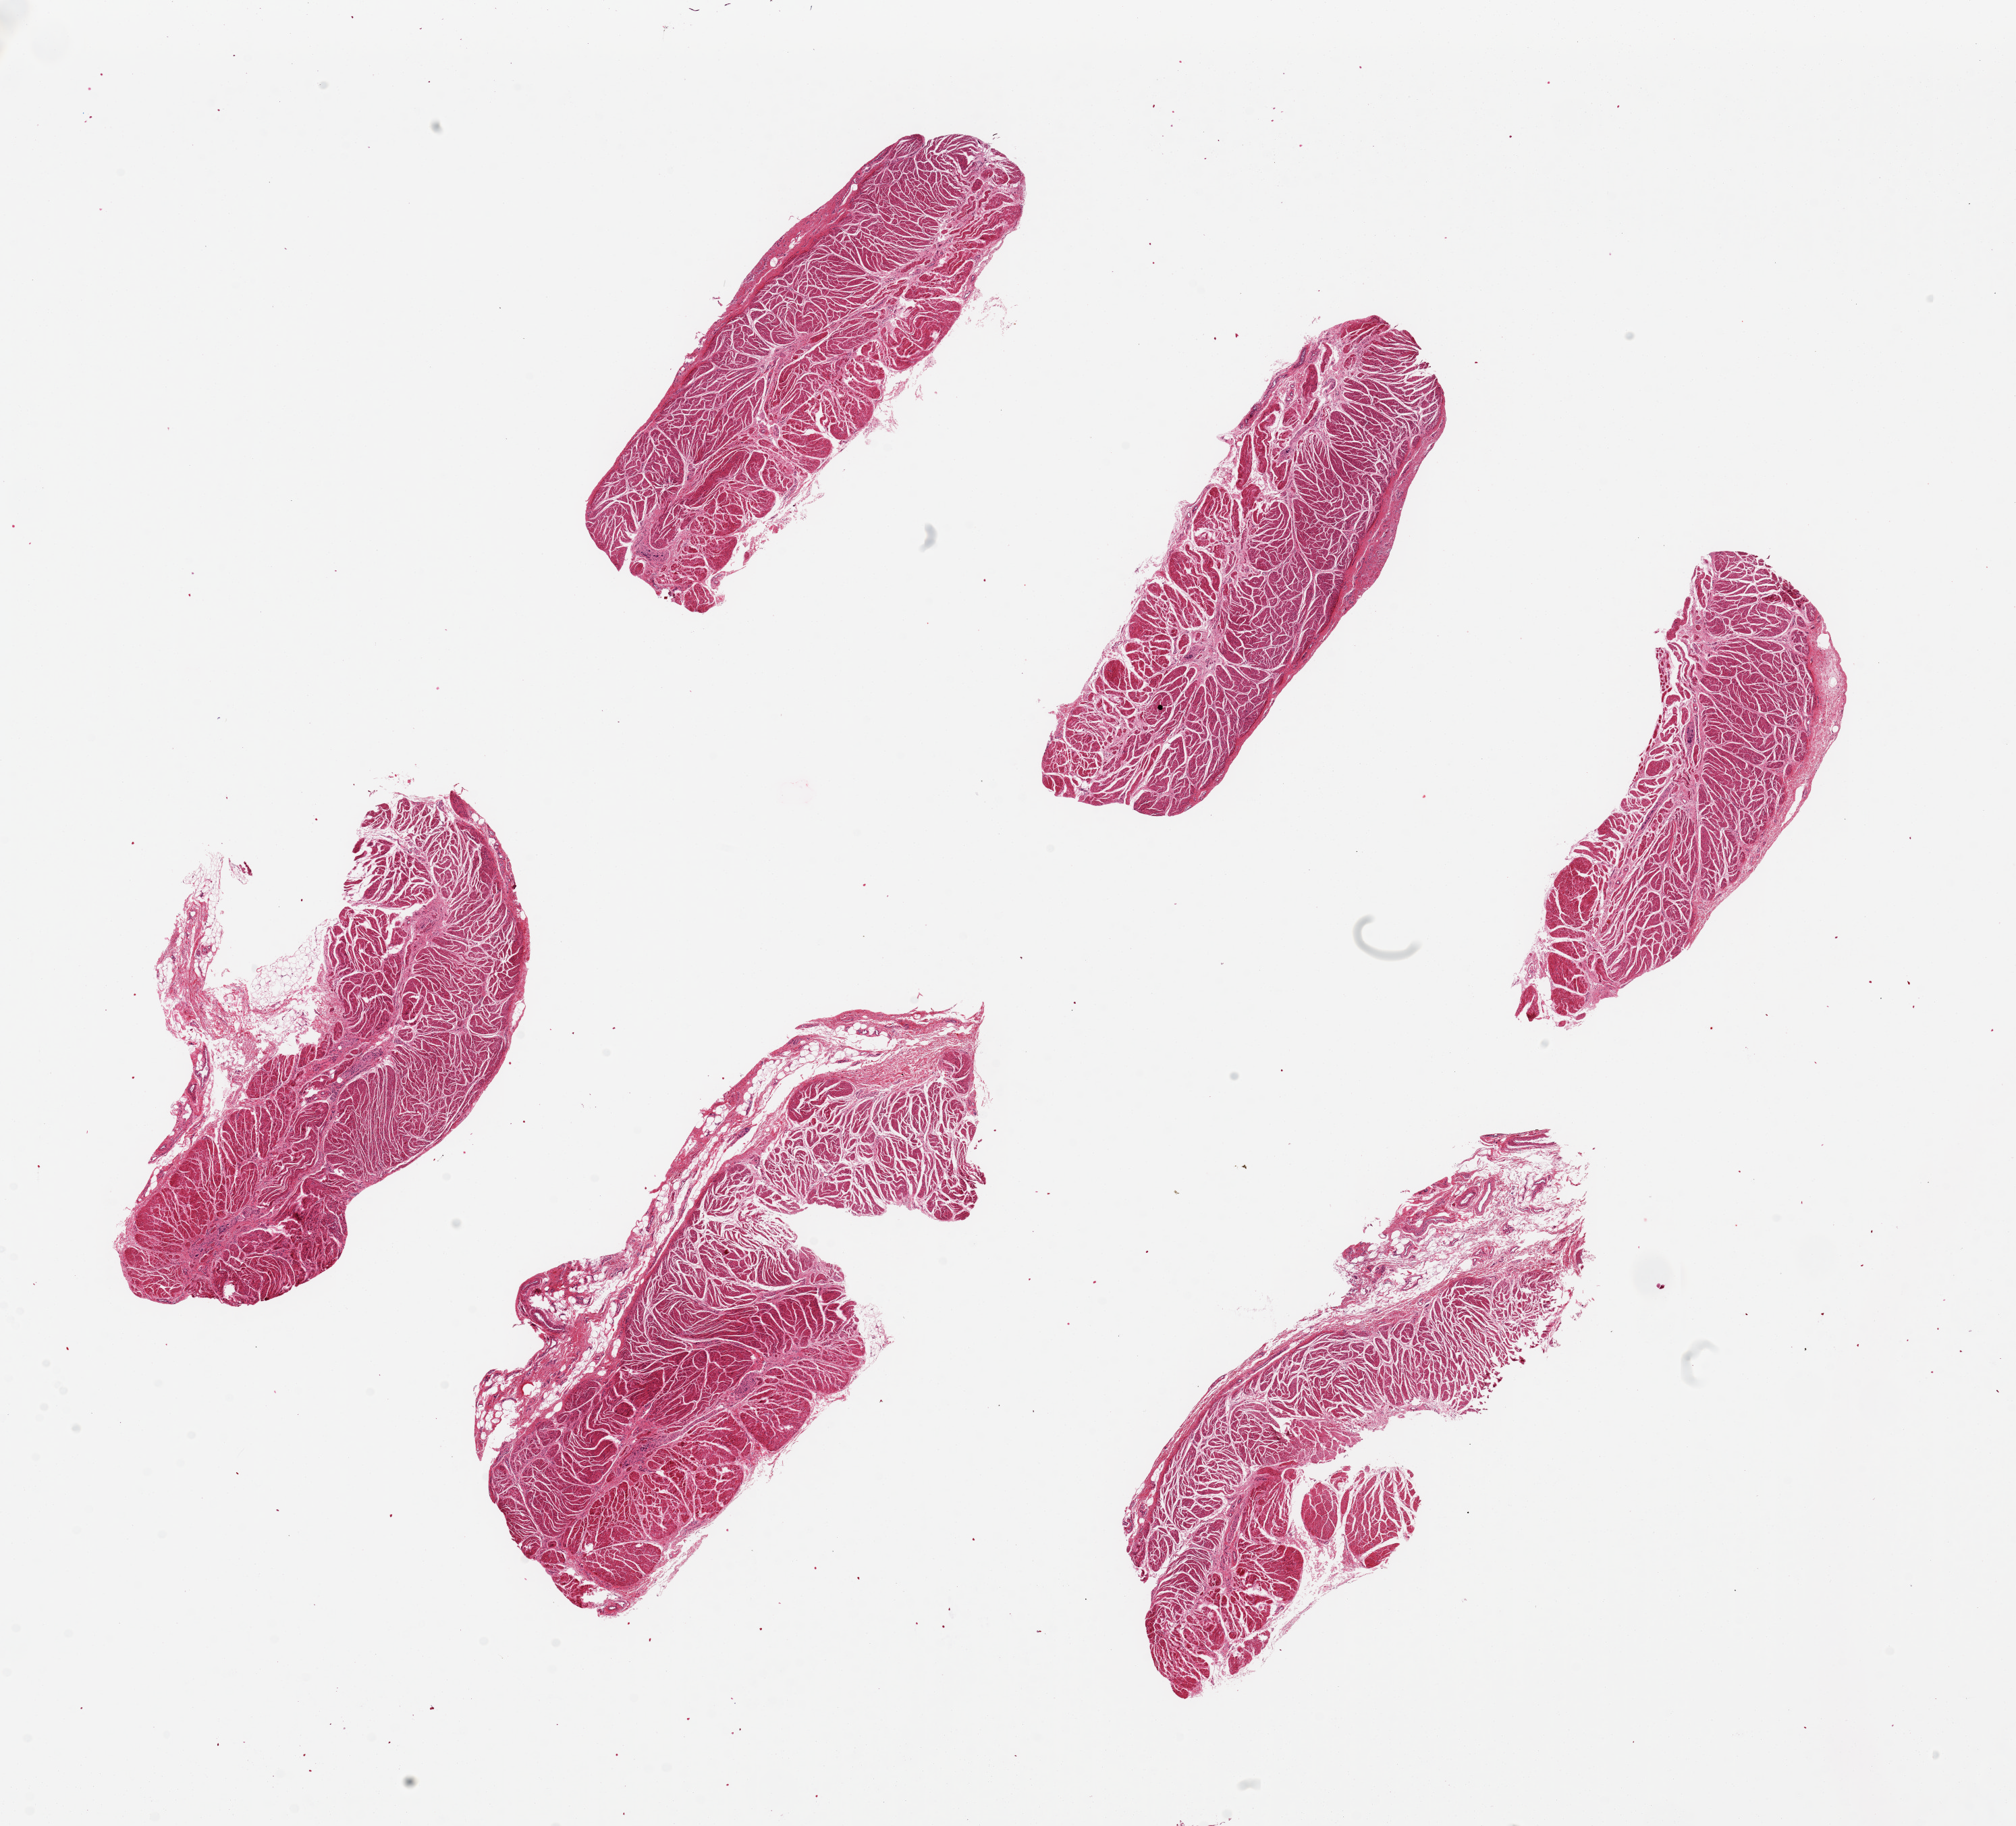
Digitized H&E-stained section — shown as a low-resolution overview of the whole scanned area (about 23.6 x 21.4 mm, acquisition: 20x scan). PAXgene-fixed paraffin-embedded (PFPE) section. Target tissue: gastroesophageal junction. Tissue donor sample. Donor: male.
• reviewer comment on this tissue sample: 6 pieces, muscle only per protocol, ~ 7x2mm